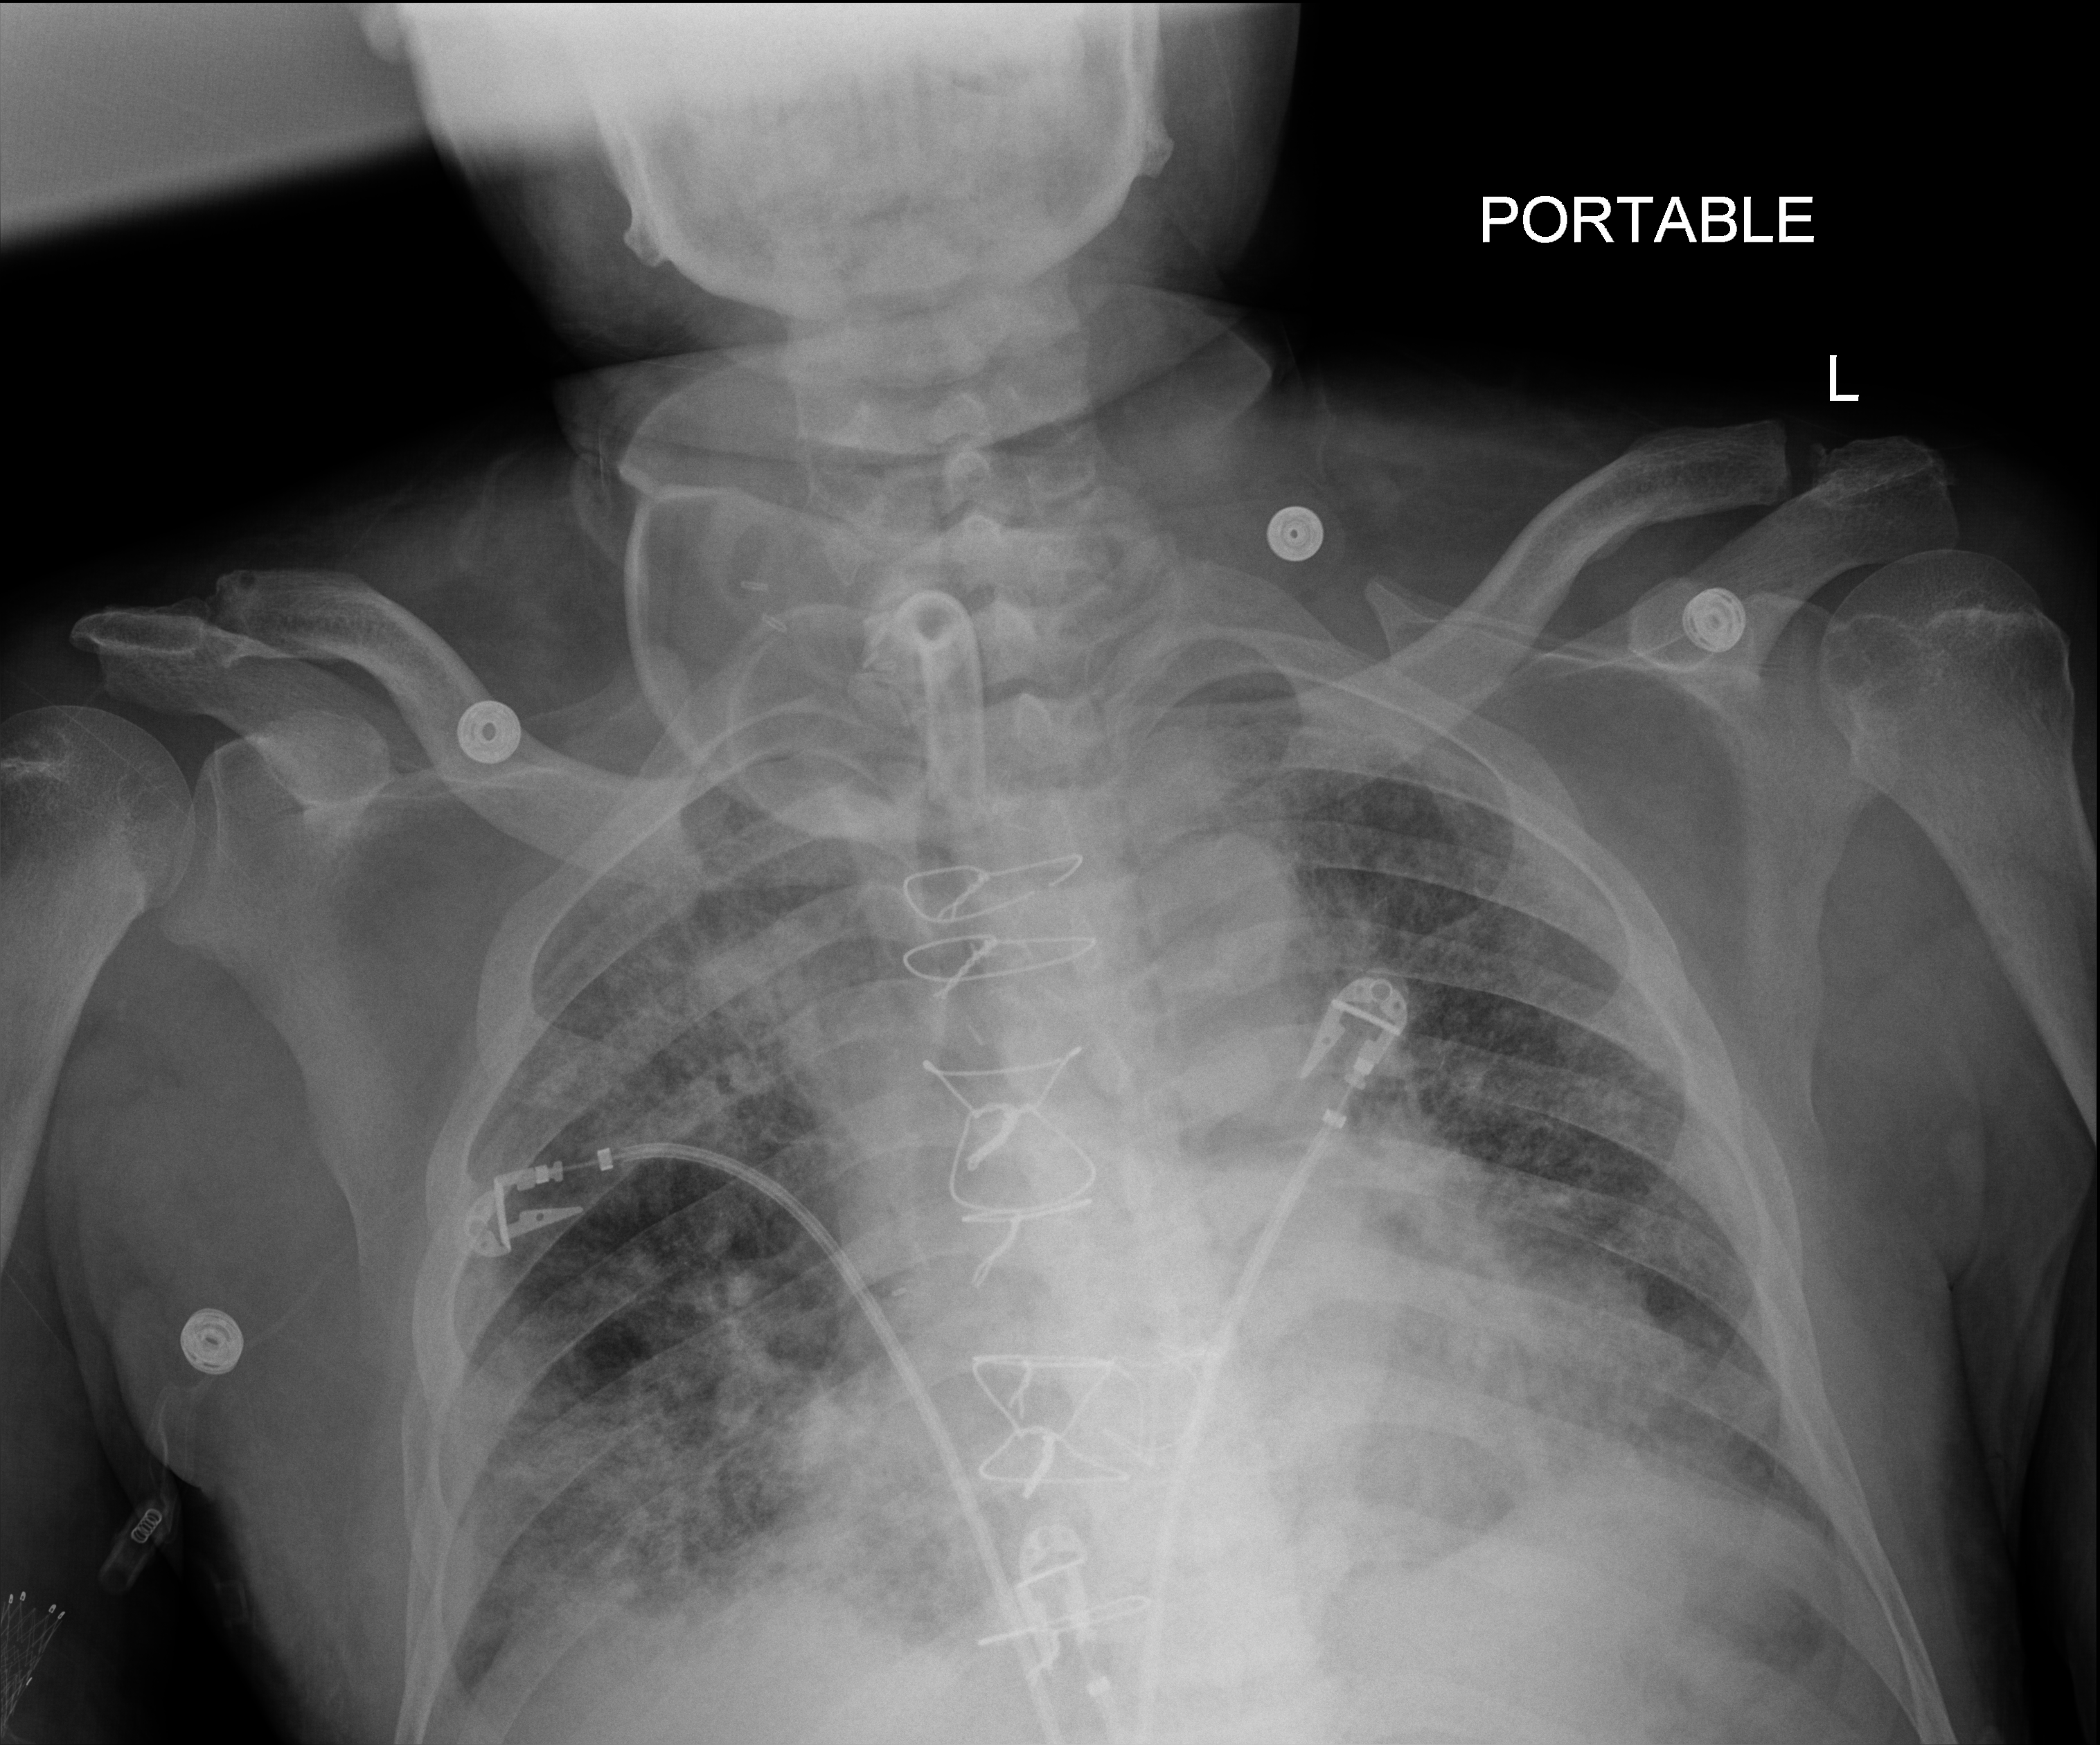
Portable chest radiograph; anteroposterior (AP) projection. Patient hospitalised with COVID-19; male, aged 60–74 years.
Admission-level facts for this patient (not findings on this image; timing relative to this image not recorded): chronic kidney disease (admission record): no; admitted to intensive care during this hospital stay: yes; mechanically ventilated during this hospital stay: yes.